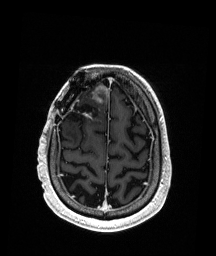
Brain MRI from a brain-tumour surgery series, one axial slice. Slice 45 of 192 in the series (ordered by position). T1-weighted post-contrast. 216 × 256 image matrix, field of view 211 × 250 mm. Case-level facts recorded for this patient, not image findings: histopathology: Astrocytoma; WHO grade: 3; IDH mutation: yes.
Structures marked on this image (manually delineated by an expert):
- previous resection cavity: box from (x=67, y=103) to (x=99, y=124) px
- tumour: (x=93, y=85)–(x=109, y=103)